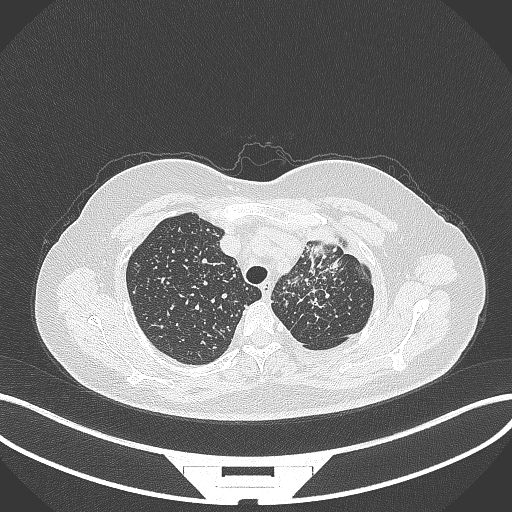
Chest CT, one axial slice; position 270 of 348 along the scan axis; lung window (W 1500 / L -600 HU); 1 mm slice thickness; 512 × 512 image matrix, field of view 400 × 400 mm. Female patient, age 49 years. From the clinical record (not read from this slice): clinical TNM (as recorded): T1c N0 M1.
Structures marked on this image (bounding box drawn by a radiologist):
- lung tumour (recorded histology: adenocarcinoma): bounding box (x1, y1, x2, y2) in pixels: (306, 223, 343, 252)